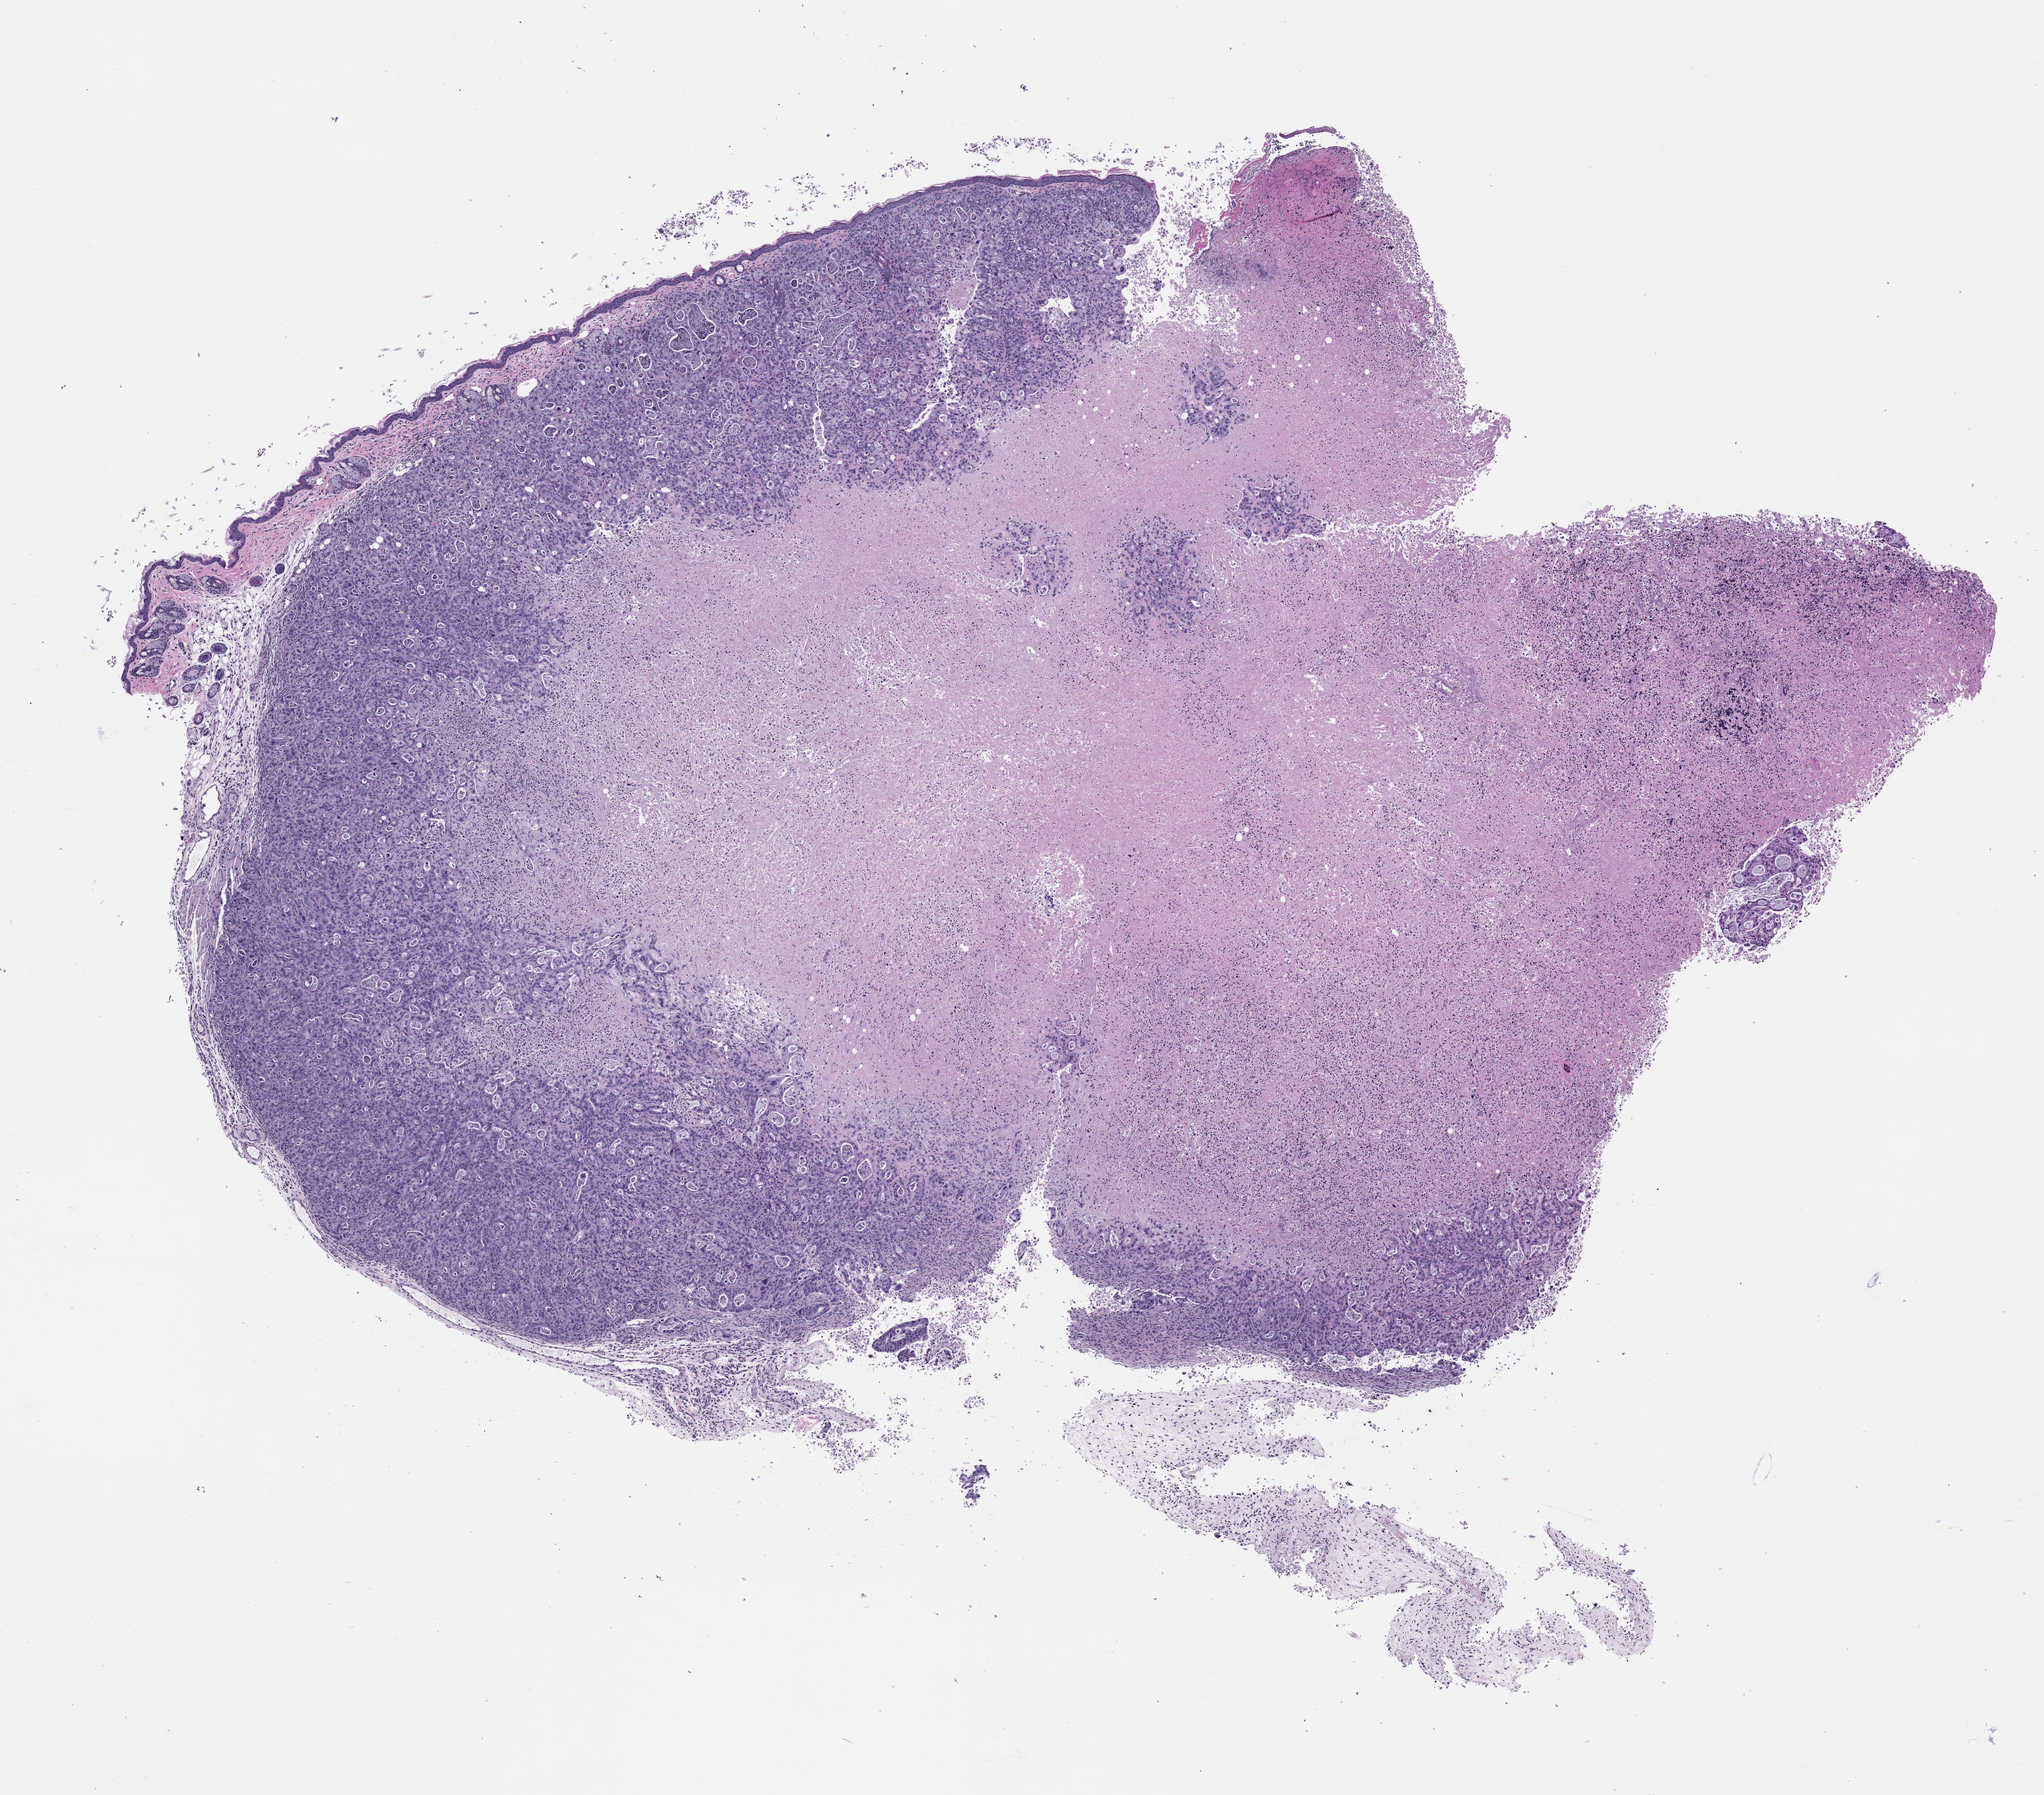
Hematoxylin and eosin (H&E) whole-slide image of a patient-derived xenograft (PDX) tumor grown in a mouse, passage 0, whole scanned area (about 10.0 x 8.8 mm) shown as a low-resolution overview. Formalin-fixed paraffin-embedded section. Originating tumor site category: pancreas.
- originating patient diagnosis: Pancreatic Adenocarcinoma